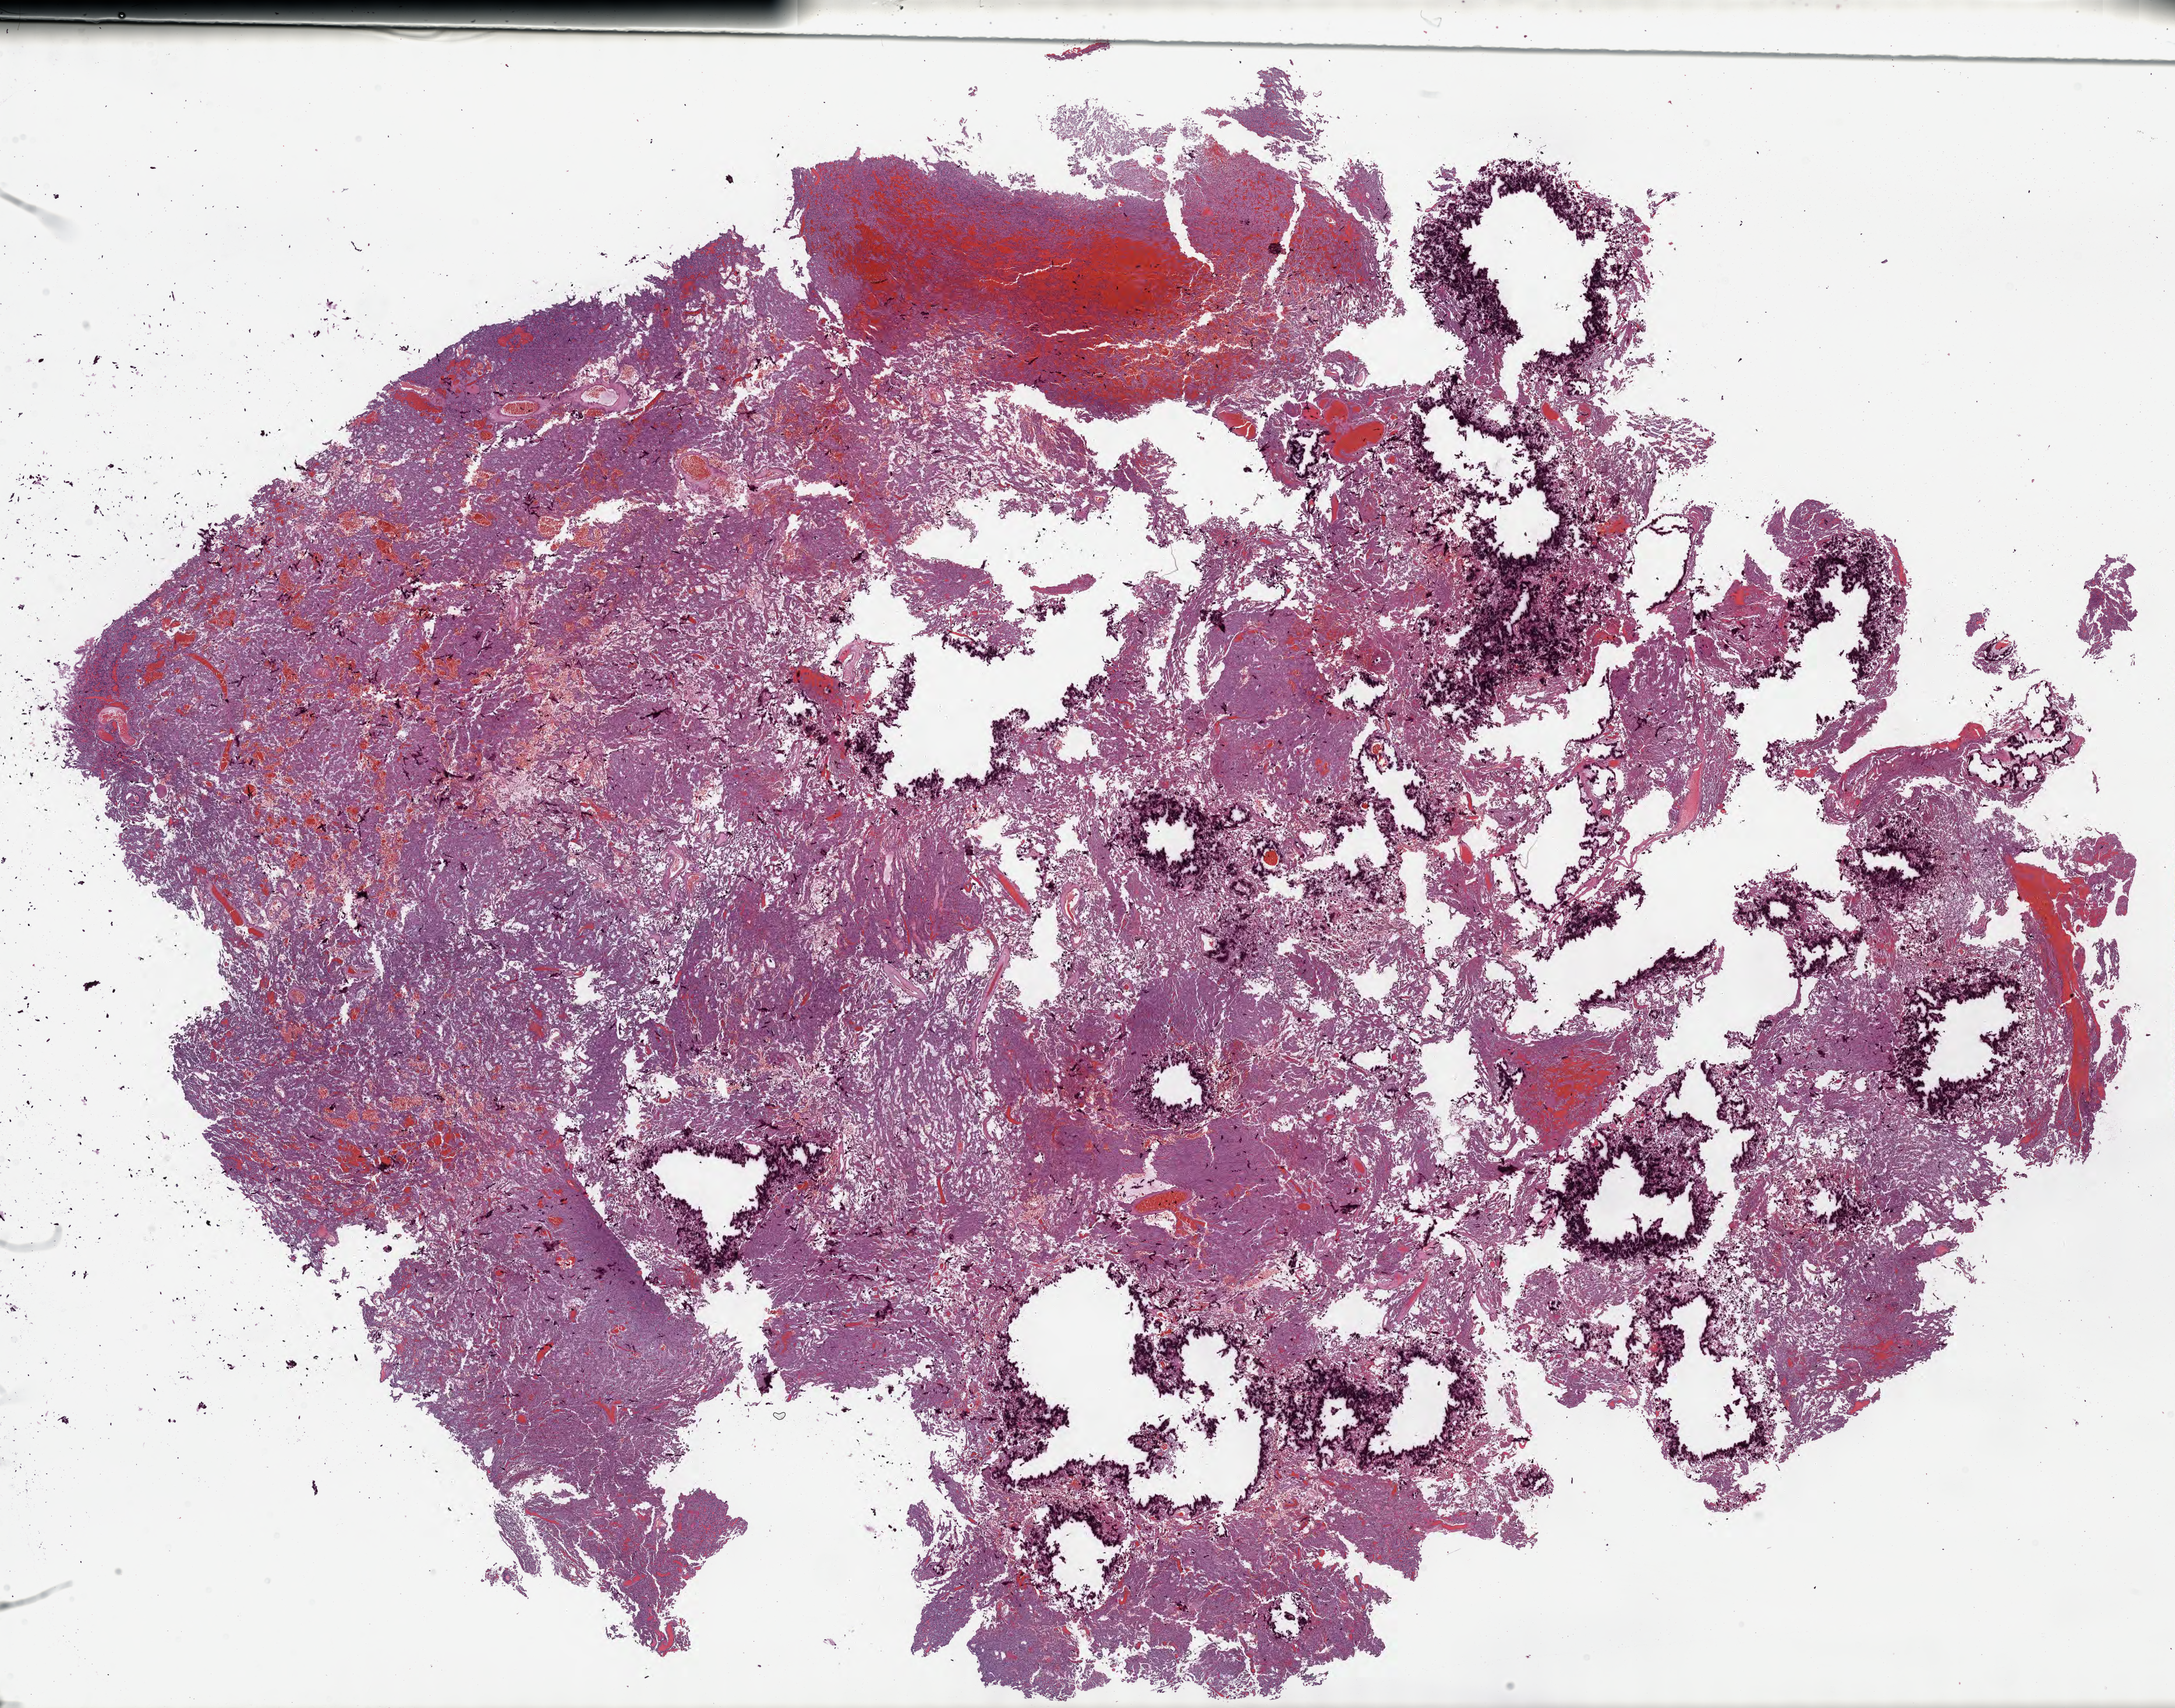
Whole-slide image, hematoxylin and eosin (H&E) stain of tumor tissue from the brain — whole scanned area (about 30.2 x 23.7 mm) shown as a low-resolution overview, FFPE section. Patient: male, age 192 months (16 years).
Diagnosis: Neoplasm, uncertain whether benign or malignant.